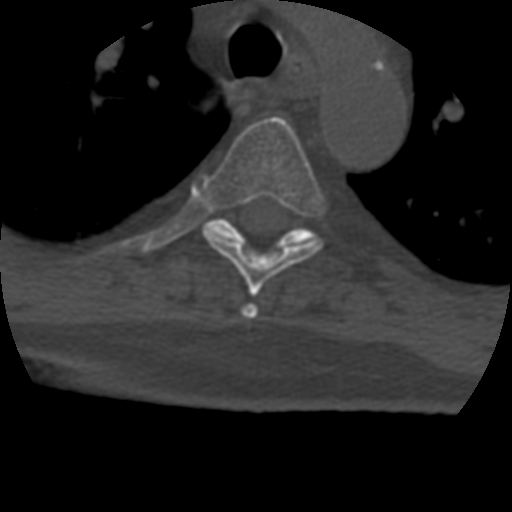
CT including the spine, one axial slice; slice 315 of 399 in the series (ordered by position); reconstruction kernel STANDARD; 120 kVp; bone window (W 1800 / L 400 HU); 1.25 mm slice thickness; 512 × 512 image matrix, field of view 160 × 160 mm. Patient age 69 years. Case-level facts recorded for this patient, not image findings: primary cancer: prostate.
Structures marked on this image (semi-automatic segmentation, software-assisted and operator-edited):
- T4 vertebra: bounding box [x1, y1, x2, y2] px = [242, 304, 258, 319]
- T5 vertebra: [202, 117, 327, 297]
- T6 vertebra: [169, 218, 316, 267]